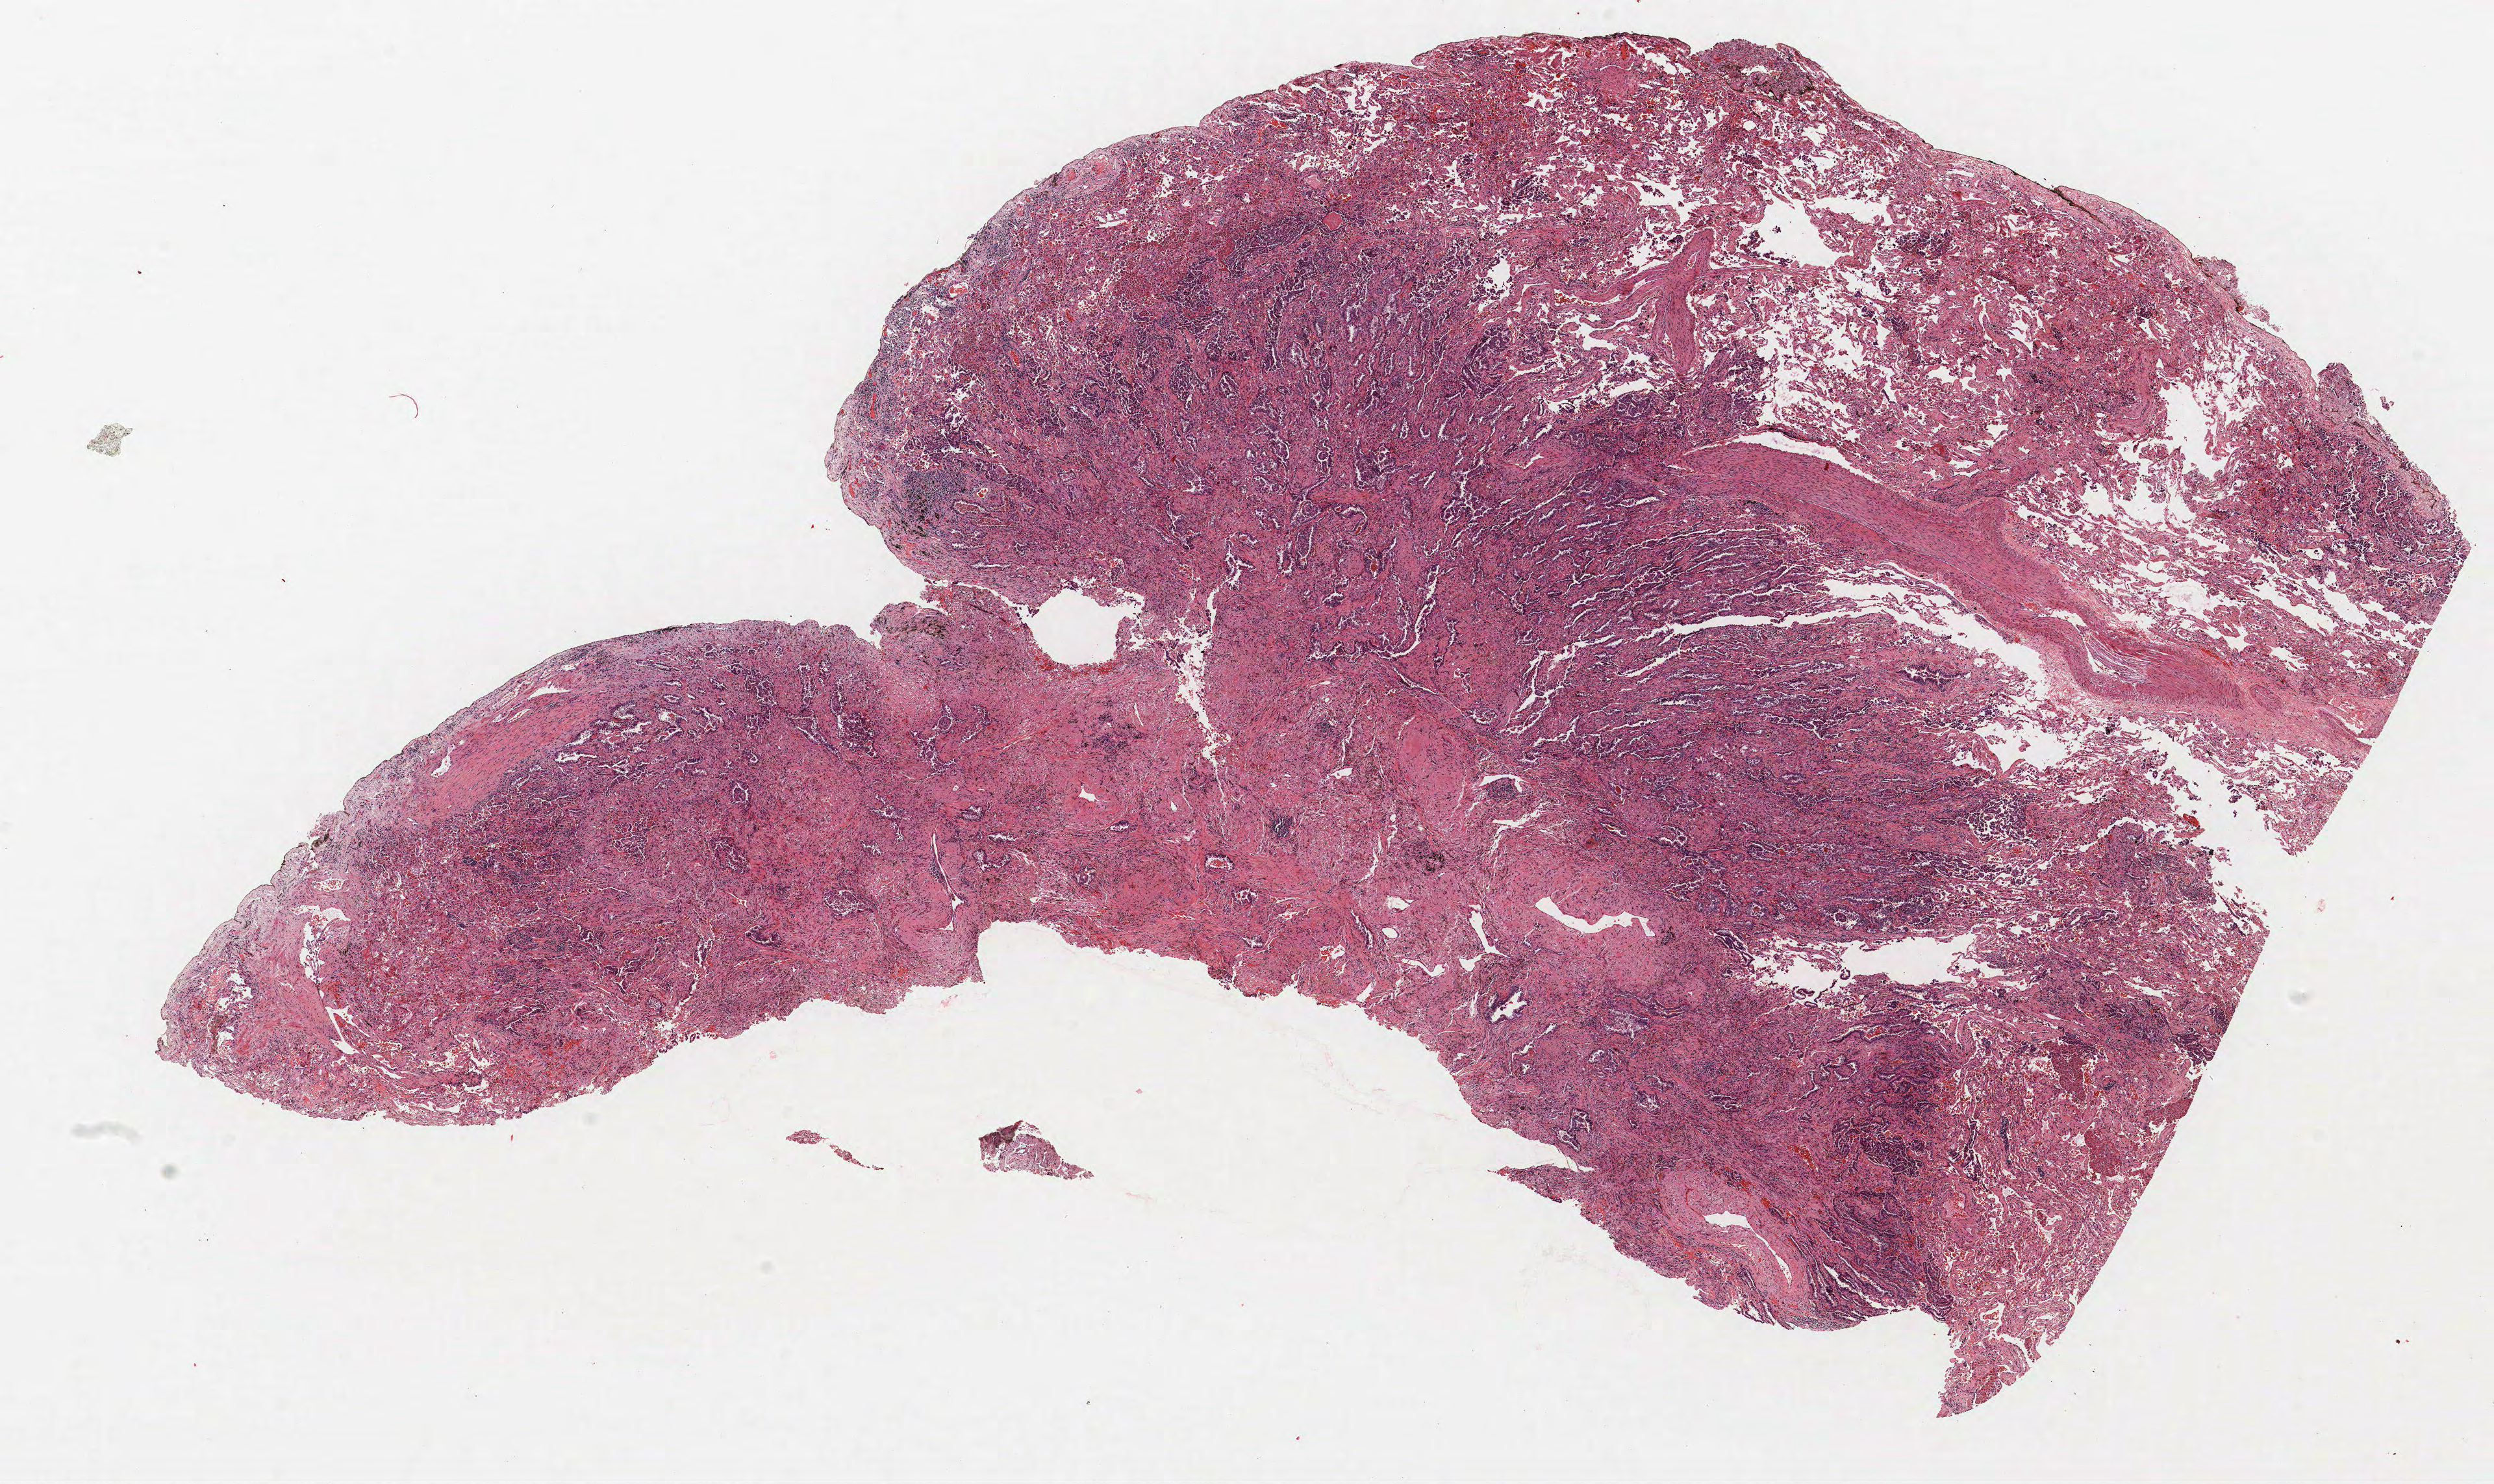
H&E whole-slide image, shown as a low-resolution overview of the whole scanned area (about 15.4 x 9.1 mm, acquisition: 40x scan); formalin-fixed paraffin-embedded (FFPE) section; lung. Female, age 55 at enrolment. Current smoker at enrolment. Grade: moderately differentiated (G2).
Stage (AJCC 6th edition): IIA. Participant's lung-cancer diagnosis: Bronchiolo-alveolar adenocarcinoma, NOS. Primary tumour location (clinical record): right upper lobe. Tumour size (pathology): 13 mm. ICD-O-3 topography: upper lobe of lung (C34.1).